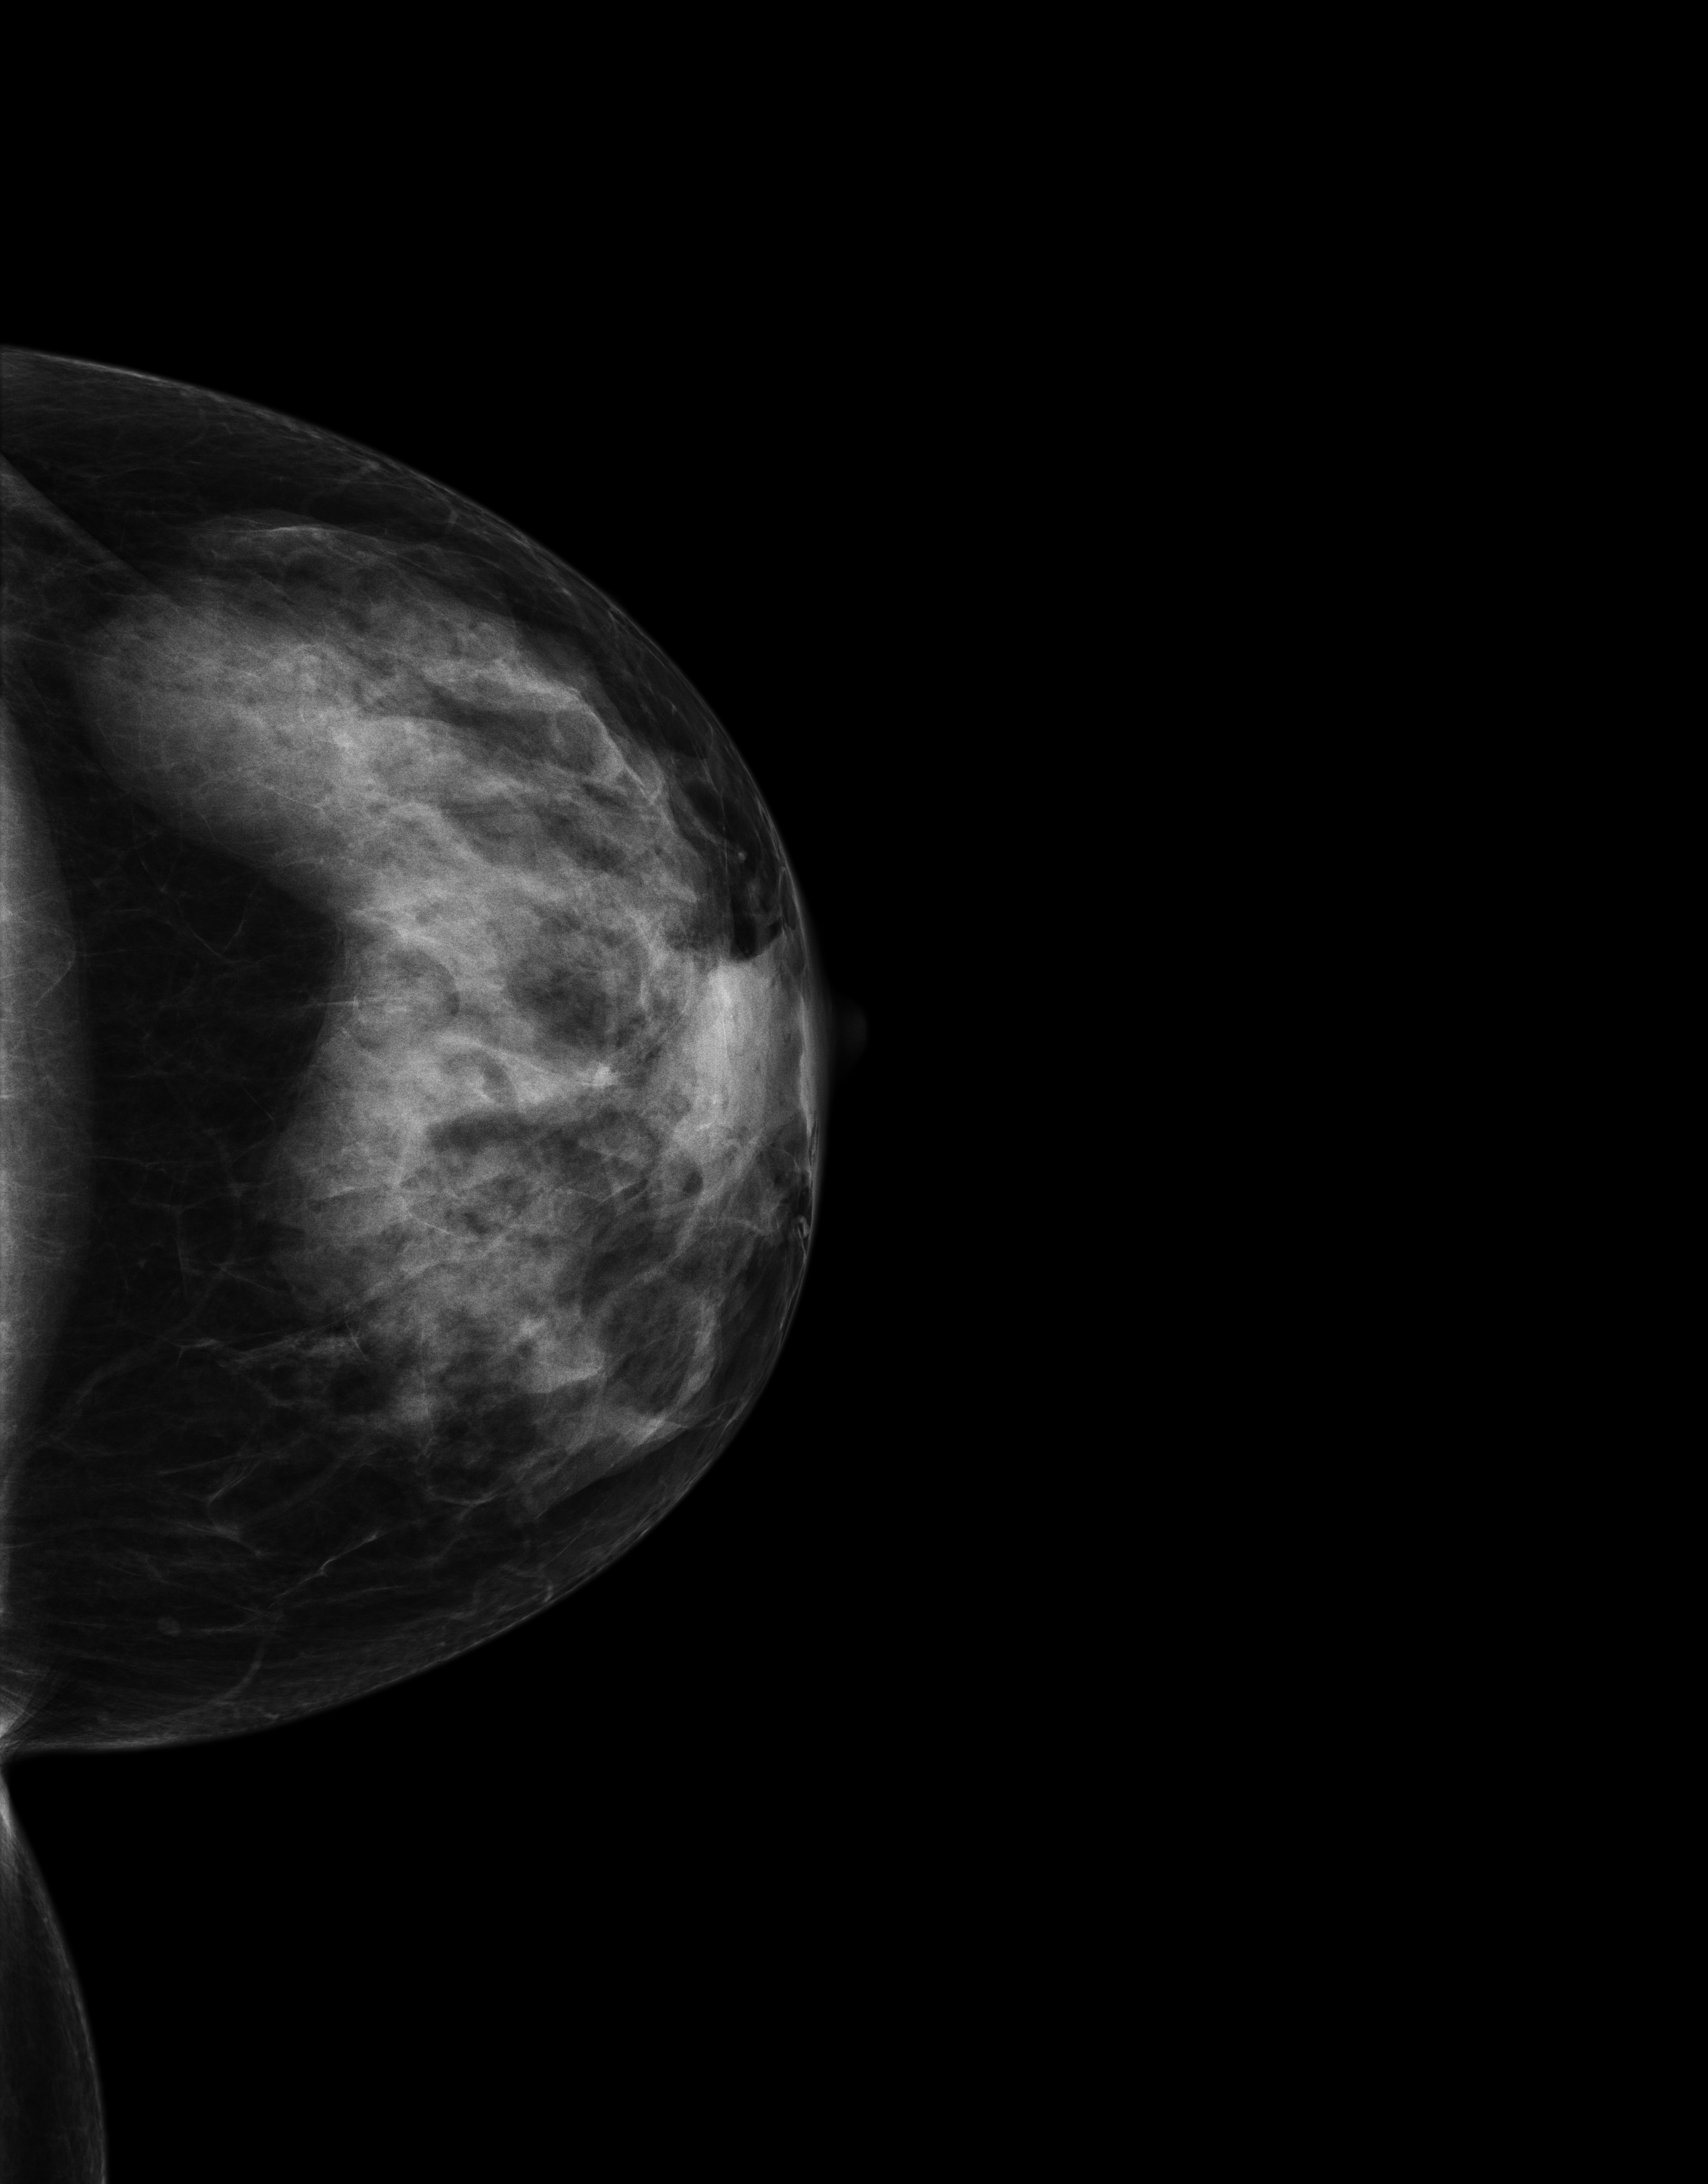
Digital mammogram (FFDM), left breast, craniocaudal (CC) view, screening examination. Female patient, age 60 years.
Breast density at the screening exam (both breasts): extremely dense (BI-RADS density category d). Final BI-RADS assessment for this screening round (tomosynthesis exam, both breasts): category 1. Recall: no recall after this screen.